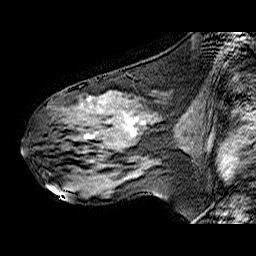
Breast MRI (dynamic contrast-enhanced), one sagittal slice. Slice 32 of 60 in the series (ordered by position). Dynamic contrast-enhanced series, time point 2 of 6 at this slice position (early post-contrast). 1.5 T. TE 6.3 ms, TR 32.9 ms. 4 mm slice thickness. 256 × 256 image matrix. Female patient. From the clinical record (not read from this slice): setting: breast cancer imaged before/during neoadjuvant chemotherapy; receptor status: HER2-positive.
Structures marked on this image (semi-automatic segmentation, software-assisted and operator-edited):
- analysis volume of interest (the breast-tissue region the enhancement analysis was run in; not a lesion): bounding box (x1, y1, x2, y2) in pixels: (47, 89, 170, 173)
- tumour enhancement mask (voxels above the 100 % enhancement threshold inside the analysis volume of interest): (85, 118, 152, 138)